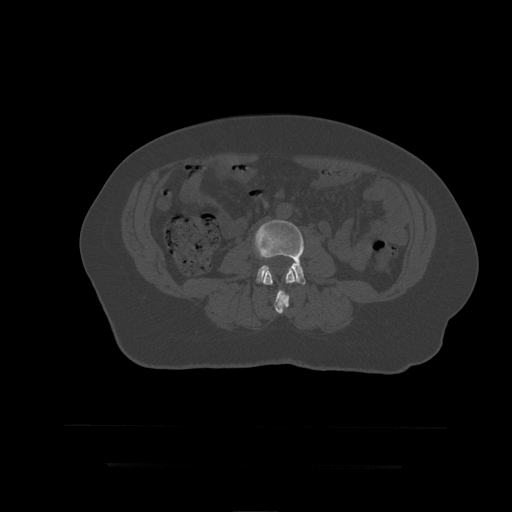
CT including the spine, one axial slice; position 109 of 399 along the scan axis; reconstruction kernel STANDARD; bone window (W 1800 / L 400 HU); 1.25 mm slice thickness; 512 × 512 image matrix, field of view 450 × 450 mm. Patient age 41 years. Case-level facts recorded for this patient, not image findings: primary cancer: breast.
Outlined on this slice (semi-automatically segmented with operator editing):
- L3 vertebra: bounding box [x1, y1, x2, y2] px = [262, 267, 296, 314]
- L4 vertebra: [255, 218, 306, 285]